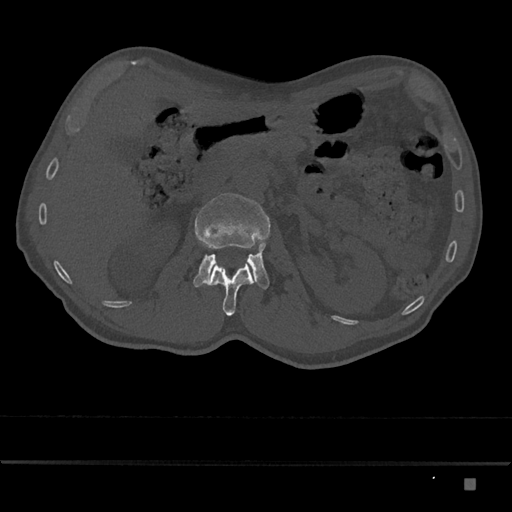
CT including the spine, one axial slice. Slice 511 of 797 in the series (ordered by position). 120 kVp. Bone window (W 1800 / L 400 HU). 0.5 mm slice thickness. 512 × 512 image matrix. Patient: male, 72 years. From the clinical record (not read from this slice): primary cancer: prostate.
Outlined on this slice (semi-automatically segmented with operator editing):
- L1 vertebra: box from (x=206, y=262) to (x=255, y=316) px
- L2 vertebra: (x=193, y=193)–(x=270, y=289)